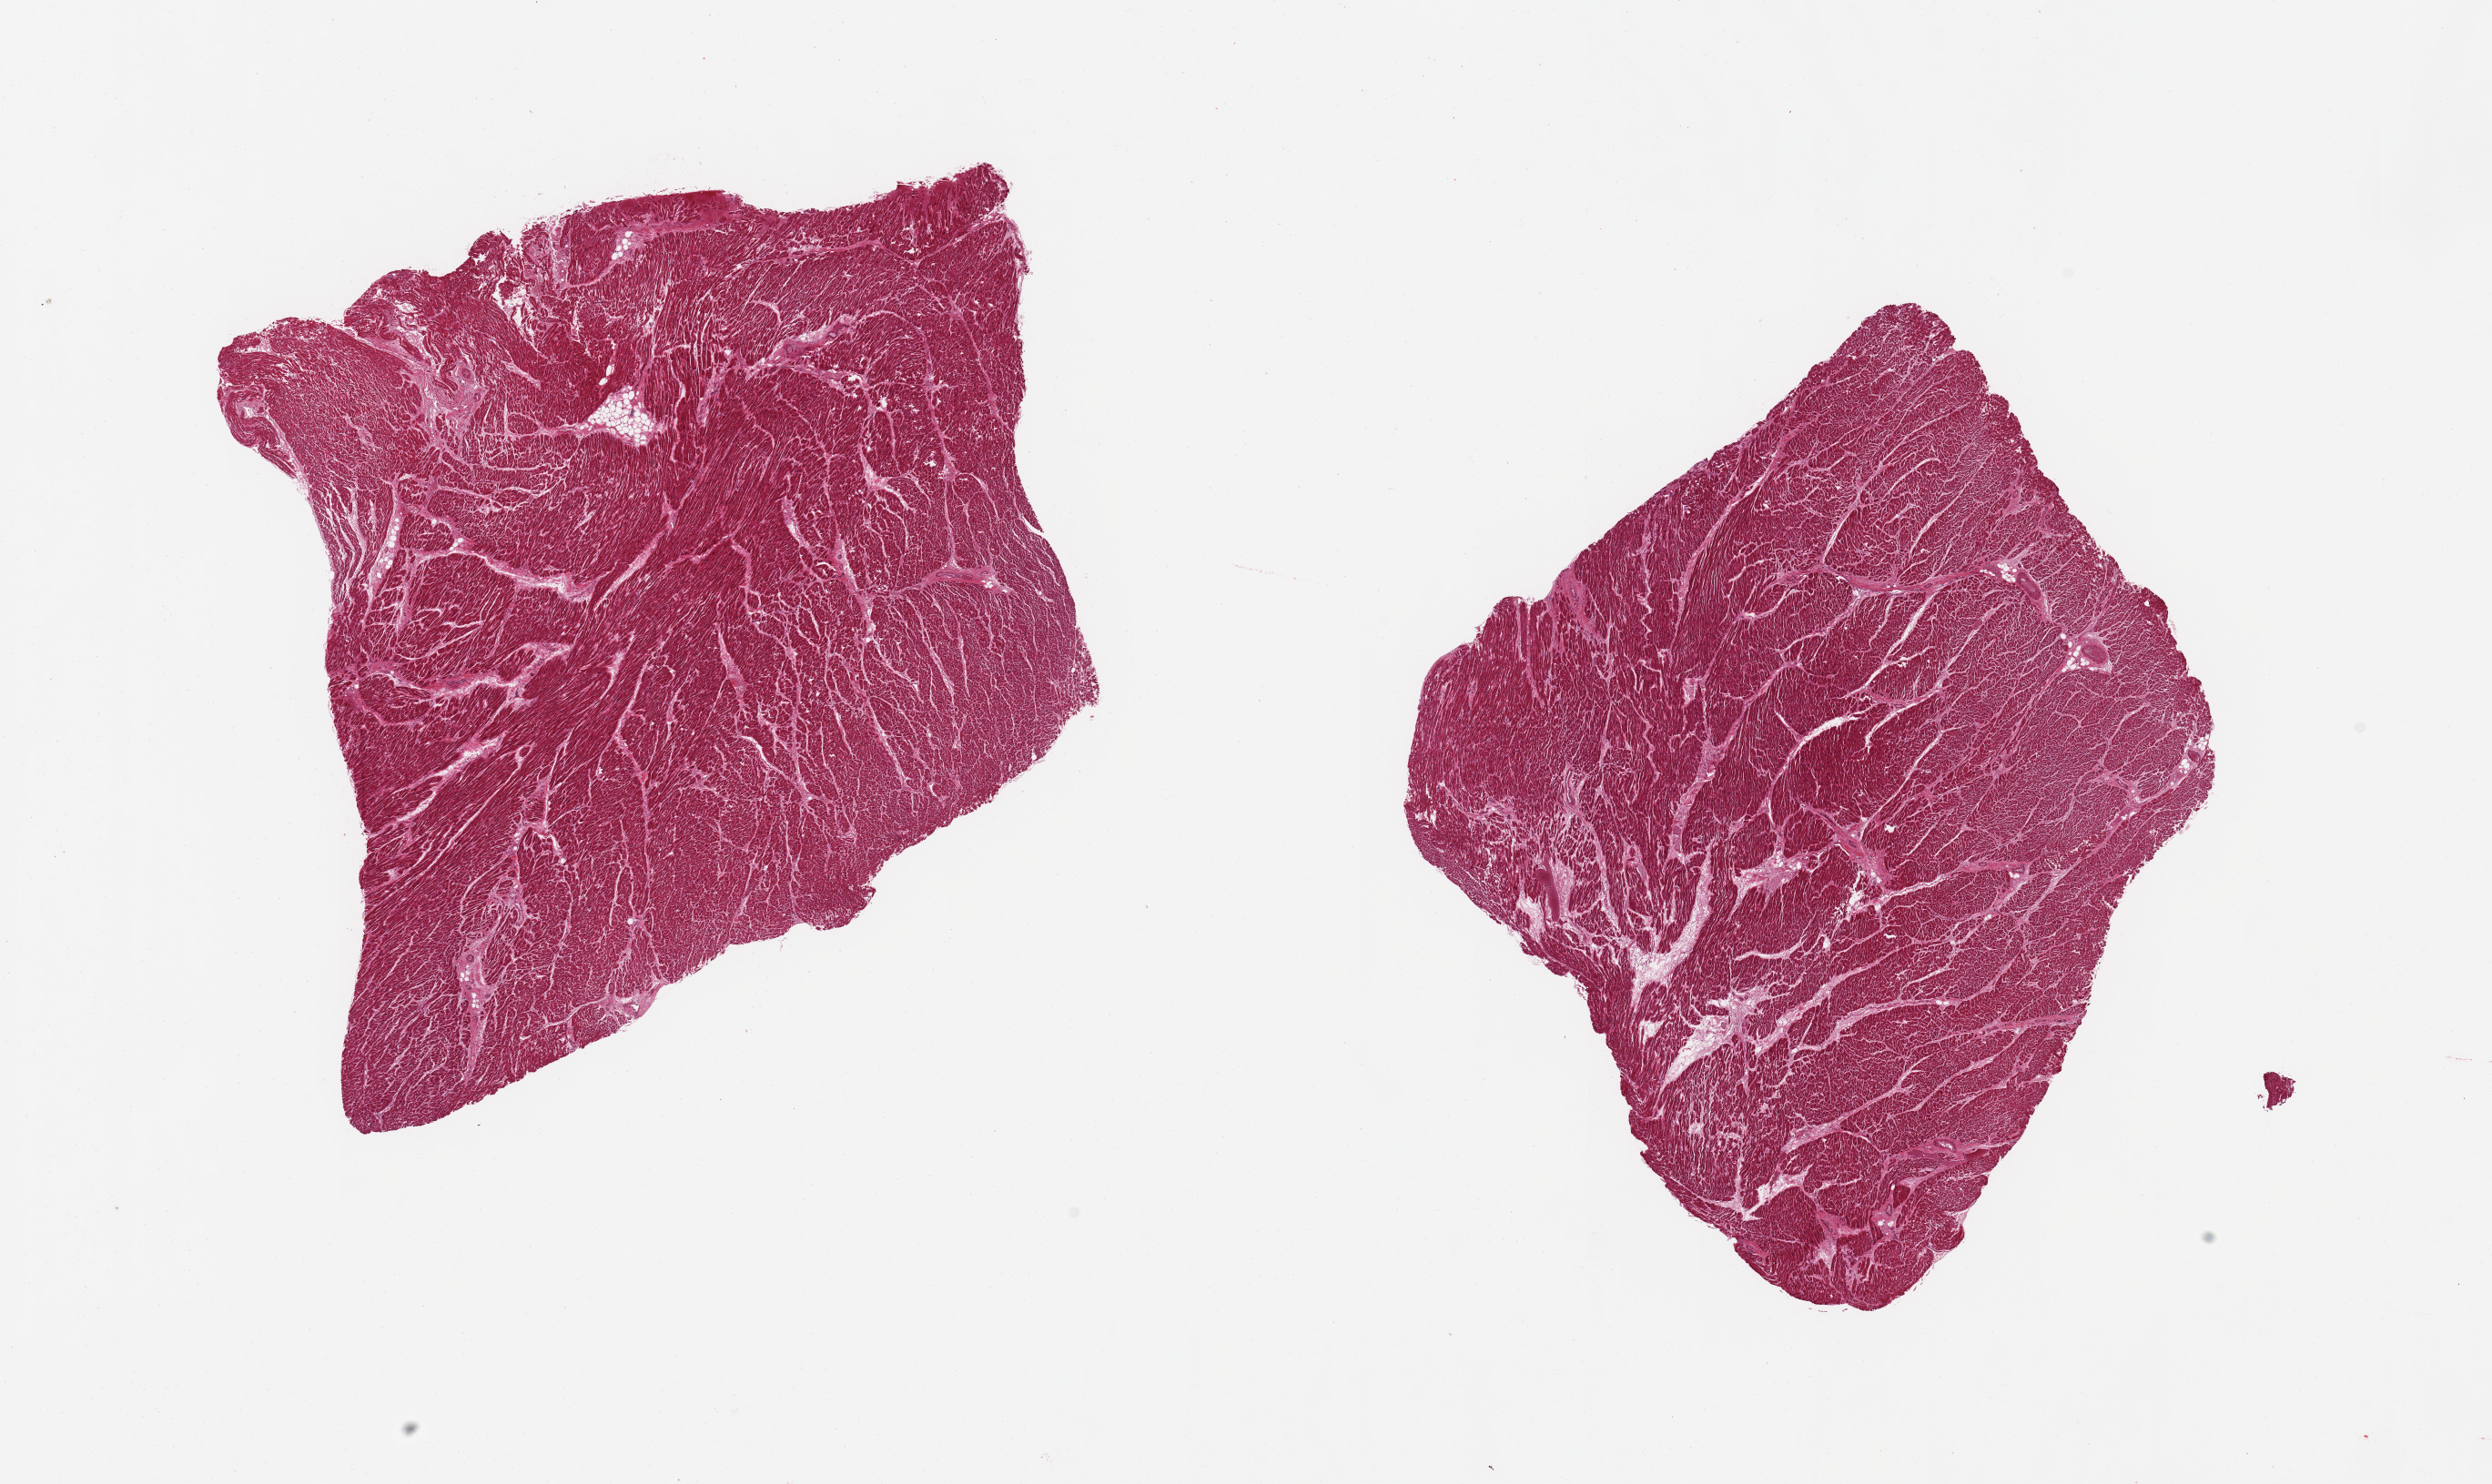
Digitized hematoxylin and eosin (H&E)-stained section, brightfield, low-resolution overview of the scanned area, about 21.7 x 12.9 mm; PAXgene-fixed paraffin-embedded (PFPE) section; target tissue: heart; tissue donor sample.
Pathologist's review note for this sample: 2 pieces; no lesions.